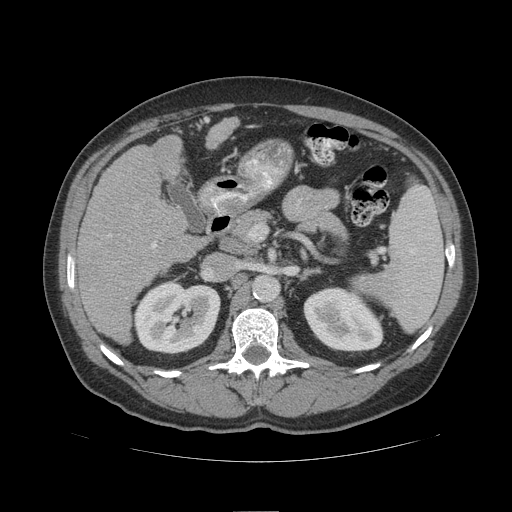
Contrast-enhanced abdominal CT (liver protocol), one axial slice; soft-tissue window (W 400 / L 40 HU); 2.5 mm slice thickness; 512 × 512 image matrix, field of view 420 × 420 mm. Case-level facts recorded for this patient, not image findings: diagnosis: hepatocellular carcinoma (patient treated with transarterial chemoembolisation; whether this scan precedes or follows treatment is not stated here); TNM stage (as recorded): Stage-IIIB; Child-Pugh class: A.
Outlined on this slice (semi-automatically segmented with operator editing):
- liver parenchyma outside the tumour (the mass and vessels are separate outlines, so this box may not span the whole liver): box from (x=78, y=117) to (x=238, y=344) px
- liver vessels: (x=152, y=243)–(x=157, y=248)